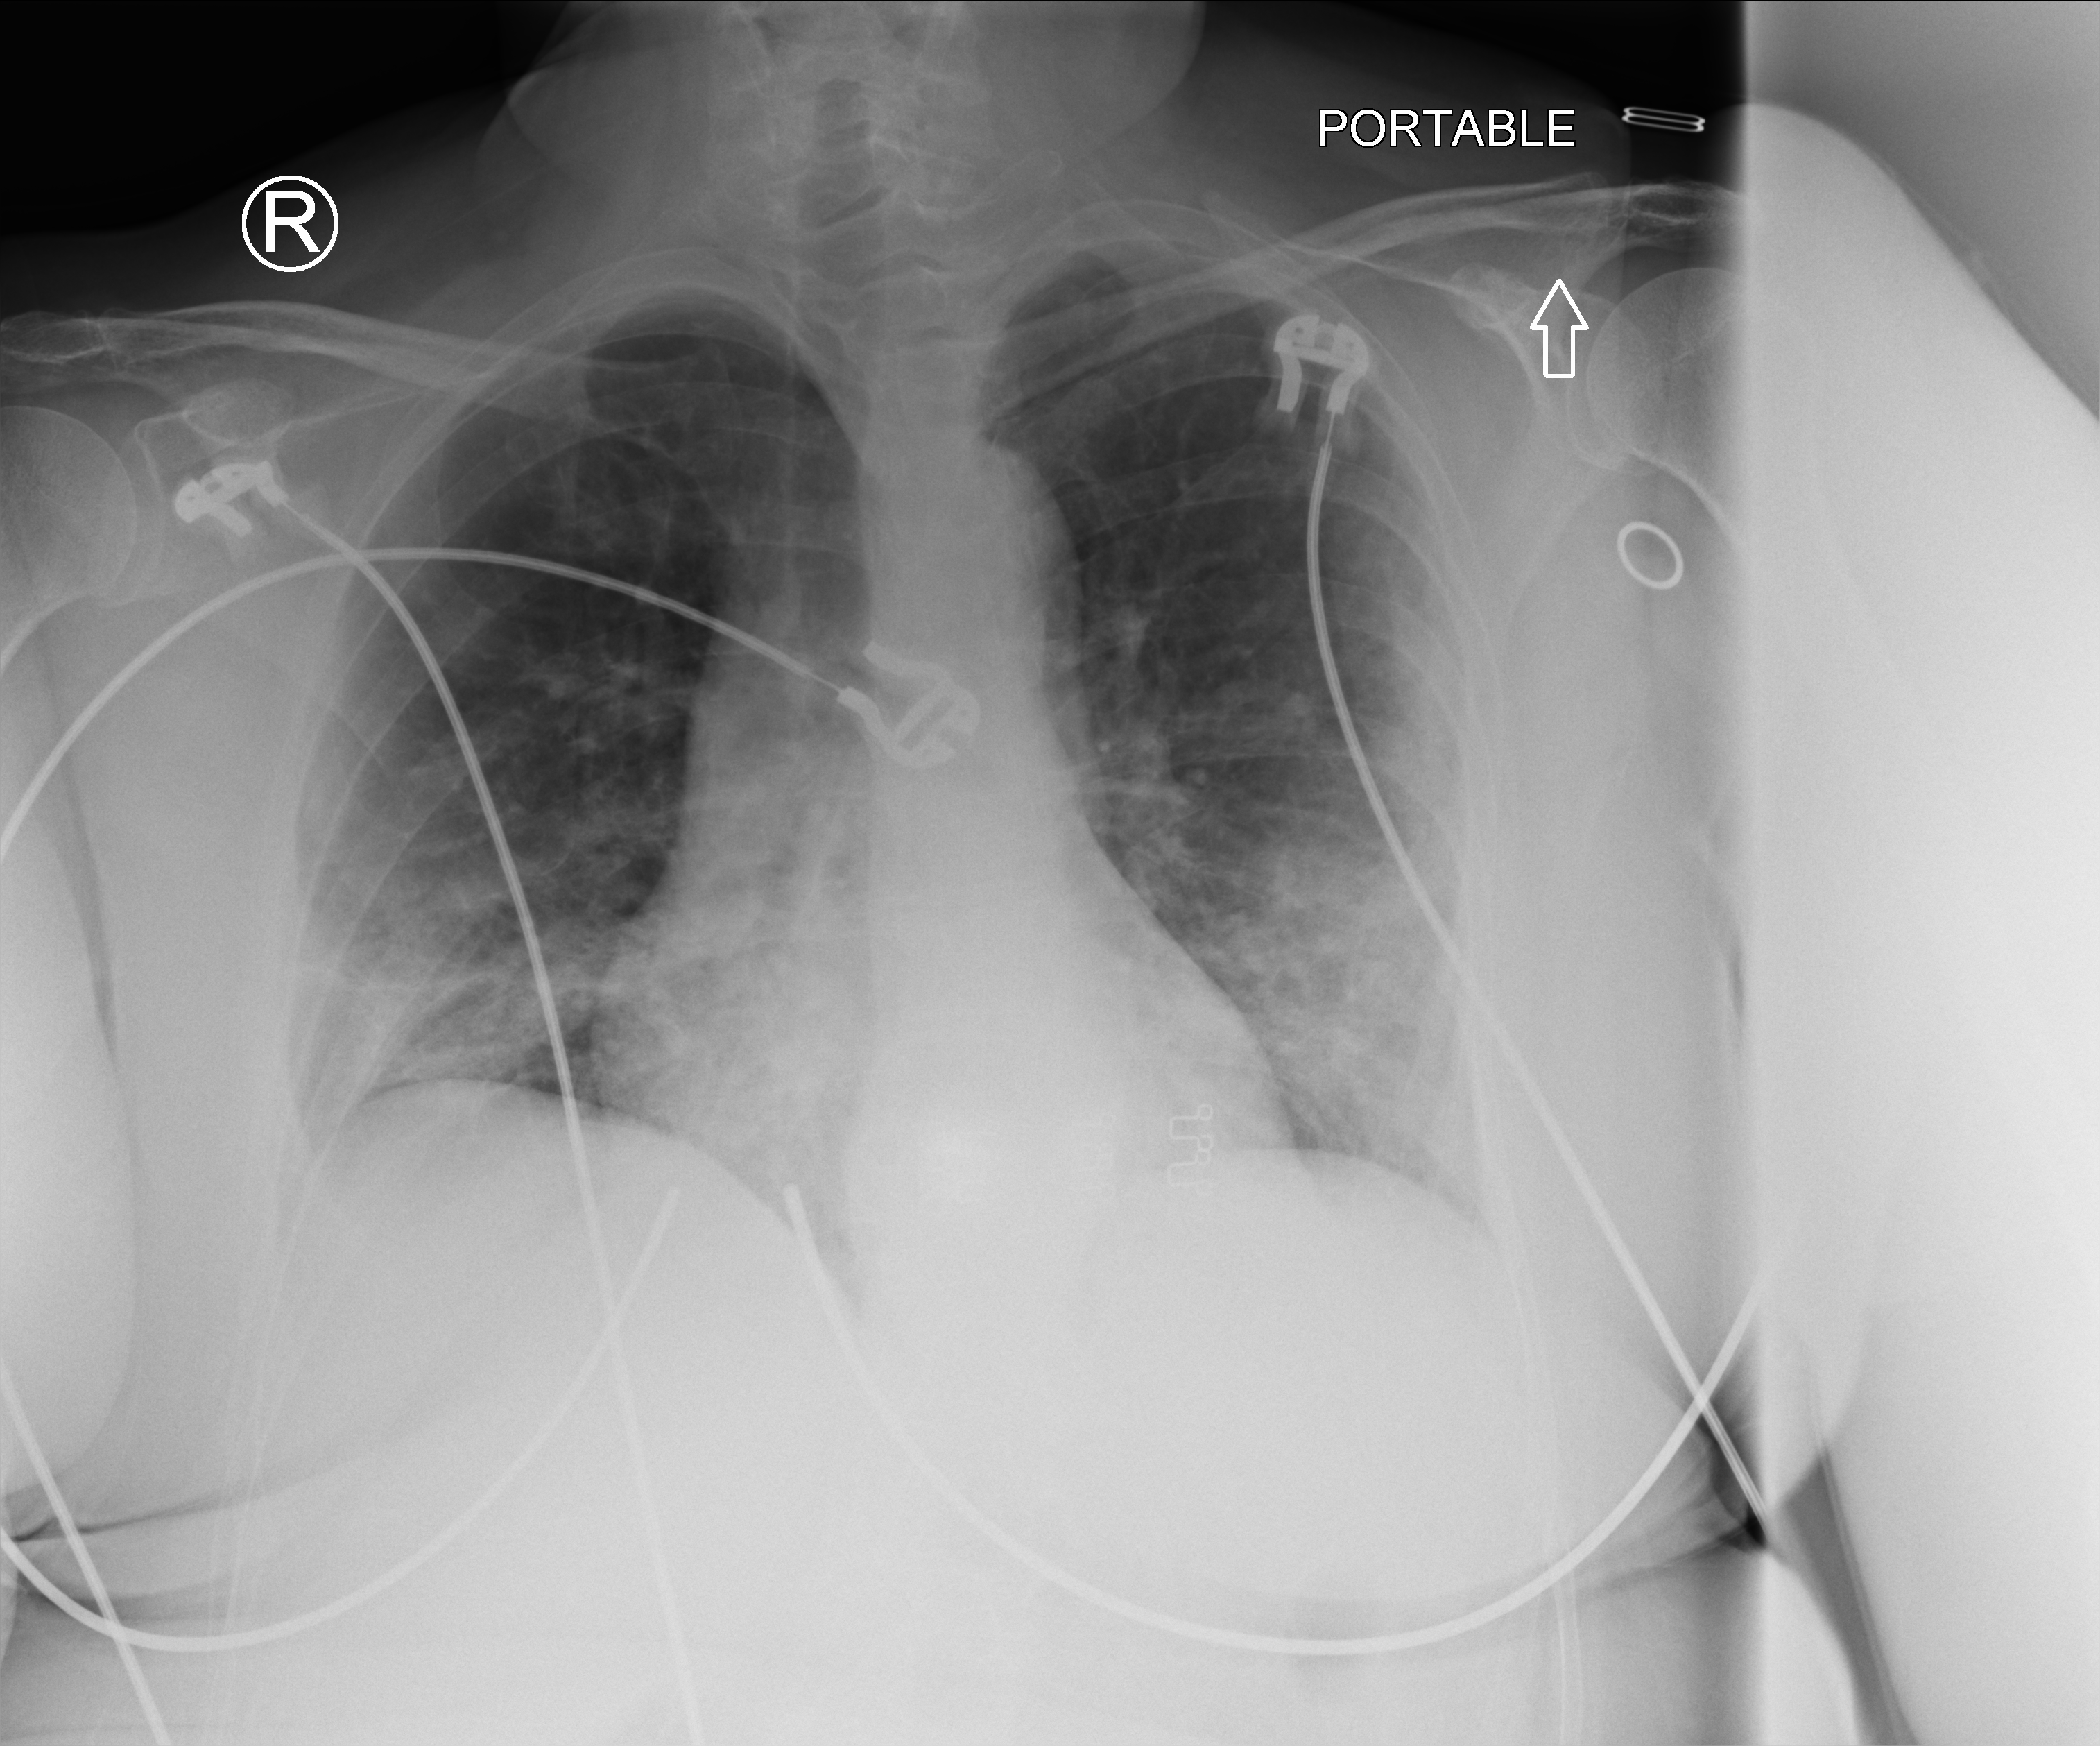
Chest X-ray (portable). Female patient hospitalised with COVID-19, age 60–74 years.
Hospital-stay facts (about this admission, not read from this image; timing relative to this image not recorded): admitted to intensive care during this hospital stay: no; mechanically ventilated during this hospital stay: no; length of hospital stay: 1 day.